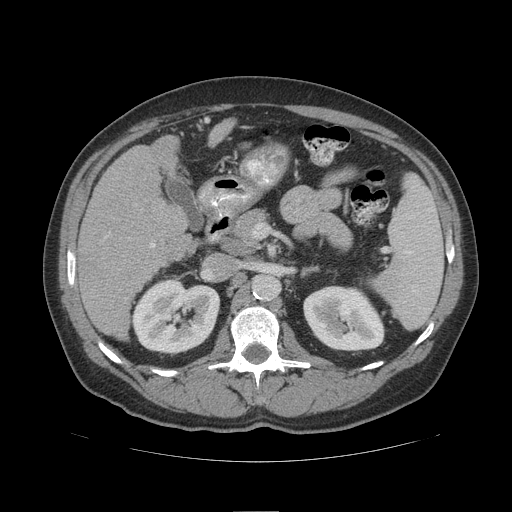
Contrast-enhanced abdominal CT (liver protocol), one axial slice. Position 54 of 109 along the scan axis. 140 kVp. Soft-tissue window (W 400 / L 40 HU). 2.5 mm slice thickness. 512 × 512 image matrix. Case-level facts recorded for this patient, not image findings: diagnosis: hepatocellular carcinoma (patient treated with transarterial chemoembolisation; whether this scan precedes or follows treatment is not stated here); TNM stage (as recorded): Stage-IIIB; Child-Pugh class: A; tumour differentiation: poorly differentiated; tumour nodularity: multinodular.
Annotated regions visible in this slice (semi-automatically segmented with operator editing):
- liver parenchyma outside the tumour (the mass and vessels are separate outlines, so this box may not span the whole liver): bounding box [x1, y1, x2, y2] px = [78, 119, 234, 340]
- liver vessels: [106, 236, 155, 247]